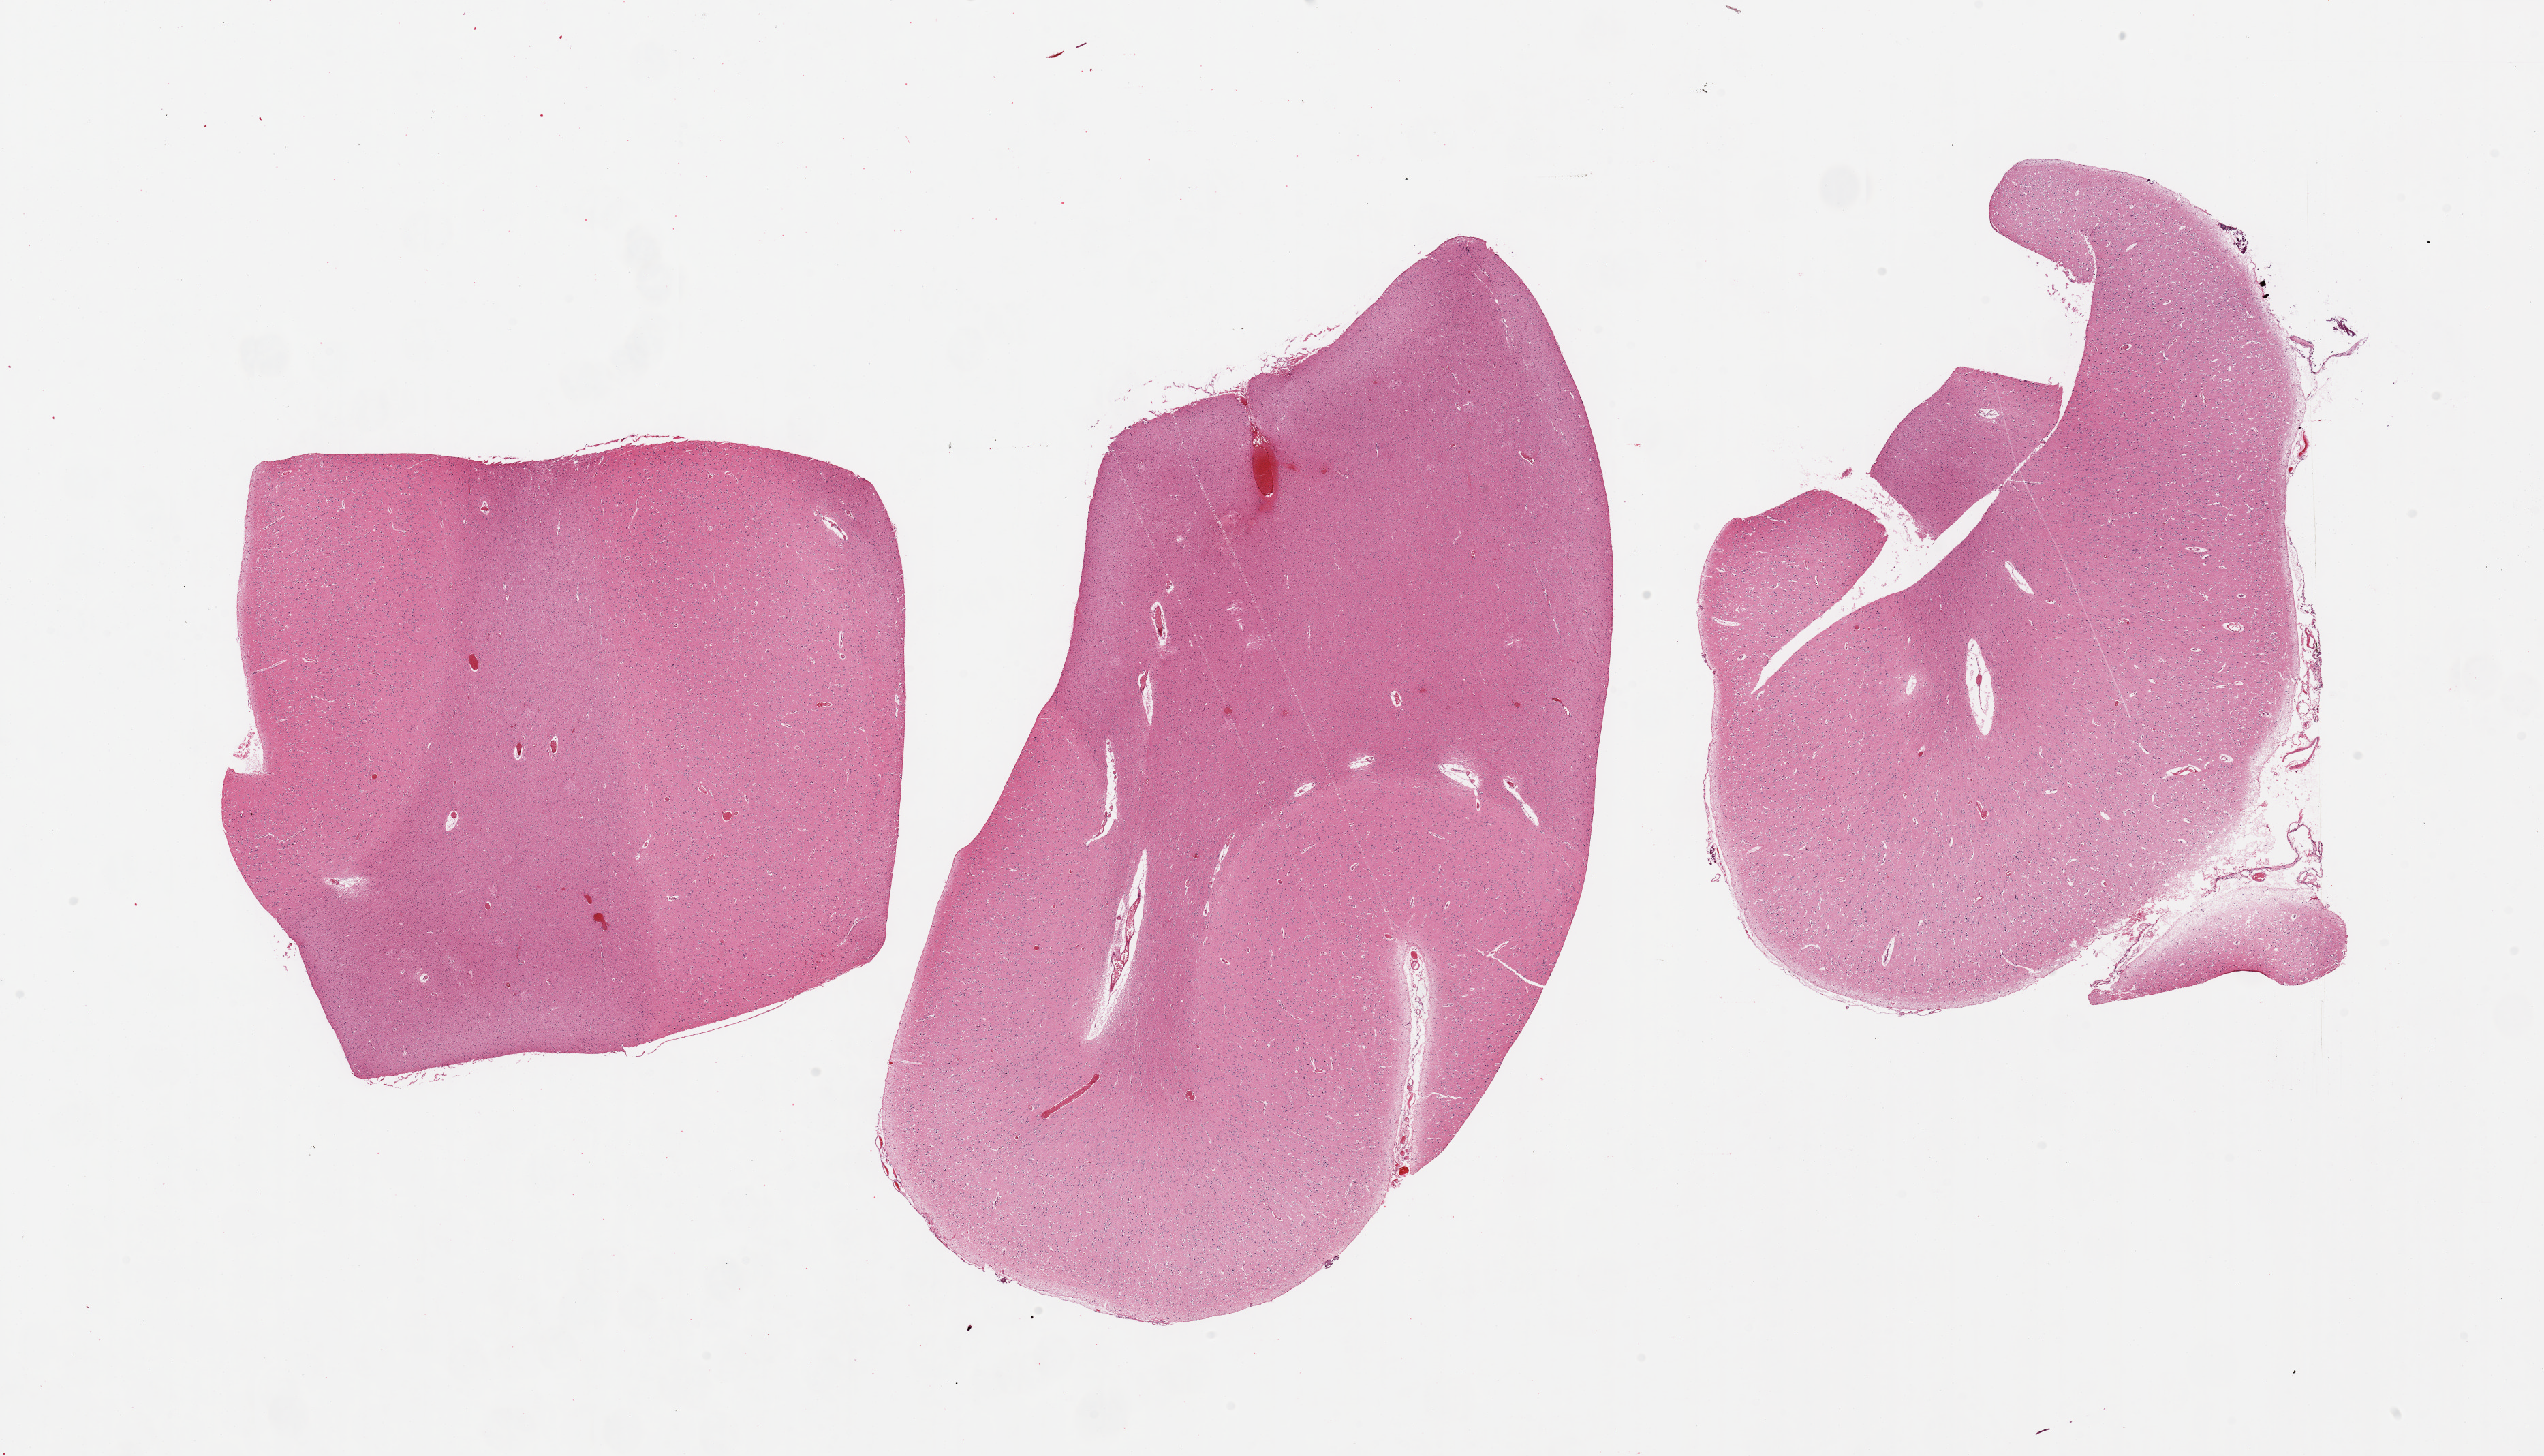
Digitized H&E-stained section, brightfield, shown as a low-resolution overview of the whole scanned area (about 29.5 x 16.9 mm, slide scanned at 20x); PAXgene-fixed paraffin-embedded (PFPE) section; target tissue: cerebral cortex; tissue donor sample. Donor sex: male.
• review note (as recorded): 3 pieces, no abnormalities